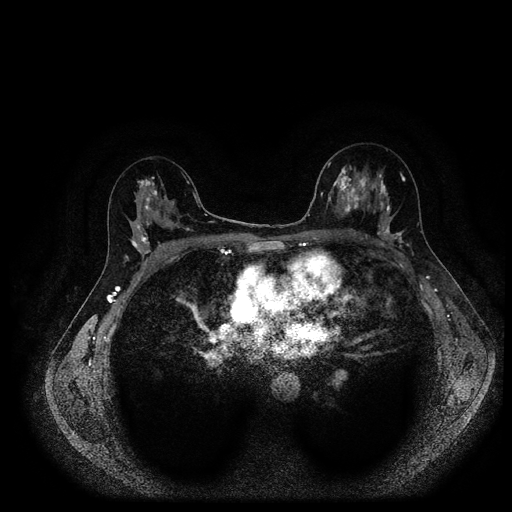
Breast MRI (dynamic contrast-enhanced, multi-phase), one axial slice. Position 59 of 116 along the scan axis. Dynamic contrast-enhanced series, time point 2 of 5 at this slice position (early post-contrast). 1.5 T. TE 2.7 ms, TR 5.4 ms. 2 mm slice thickness. 512 × 512 image matrix, field of view 340 × 340 mm. Patient: female, 40 years.
Annotated regions visible in this slice (semi-automatic segmentation, software-assisted and operator-edited):
- breast lesion (labelled 'tumour' in the annotation; benign lesions carry a separate 'benign' label): bounding box (x1, y1, x2, y2) in pixels: (336, 173, 372, 217)